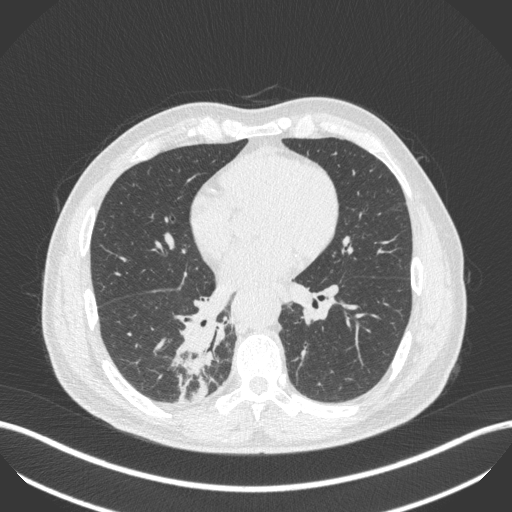
Chest CT, one axial slice. Position 214 of 451 along the scan axis. Reconstruction kernel B31f. Lung window (W 1500 / L -600 HU). 1 mm slice thickness. 512 × 512 image matrix, field of view 400 × 400 mm. Patient: male, 61 years. From the clinical record (not read from this slice): clinical TNM (as recorded): T1 N0 M0; histopathological grade: G3.
Outlined on this slice (rectangle marked by the reading radiologist):
- lung tumour (recorded histology: small cell carcinoma): bounding box (x1, y1, x2, y2) in pixels: (179, 318, 223, 398)